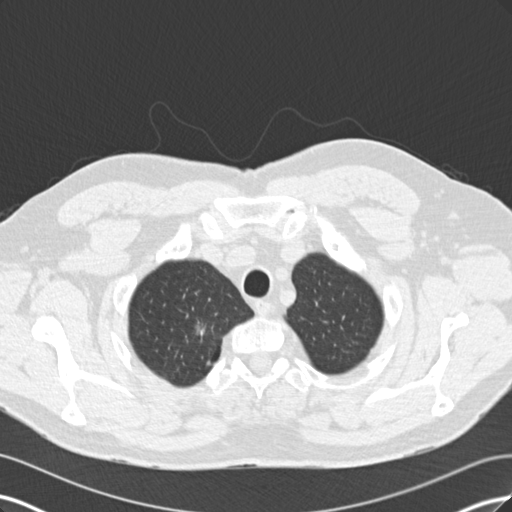
Chest CT (low-dose screening protocol), one axial image; first (baseline) screen; lung window (W 1500 / L -600 HU); 2 mm slice thickness; standard (soft-tissue) reconstruction kernel (B30f); slice 20 of 171 in the series; 512 × 512 image matrix. Male participant, aged 56 years at enrolment.
Expert-annotated lung lesion, bounding box [x1, y1, x2, y2] px = [175, 310, 224, 354]. Reader record for this screening exam (exam-level; its link to the box is not recorded): non-calcified nodule or mass ≥4 mm, right upper lobe, 14 × 8 mm, spiculated (stellate) margins. Official screen result: positive, change unspecified: nodule(s) >= 4 mm or enlarging nodule(s), mass(es), or other non-specific abnormalities suspicious for lung cancer. Lung cancer was diagnosed 146 days after this screen: adenocarcinoma, NOS, right upper lobe, poorly differentiated (G3), stage IA (AJCC 6th edition), 12 mm at pathology.